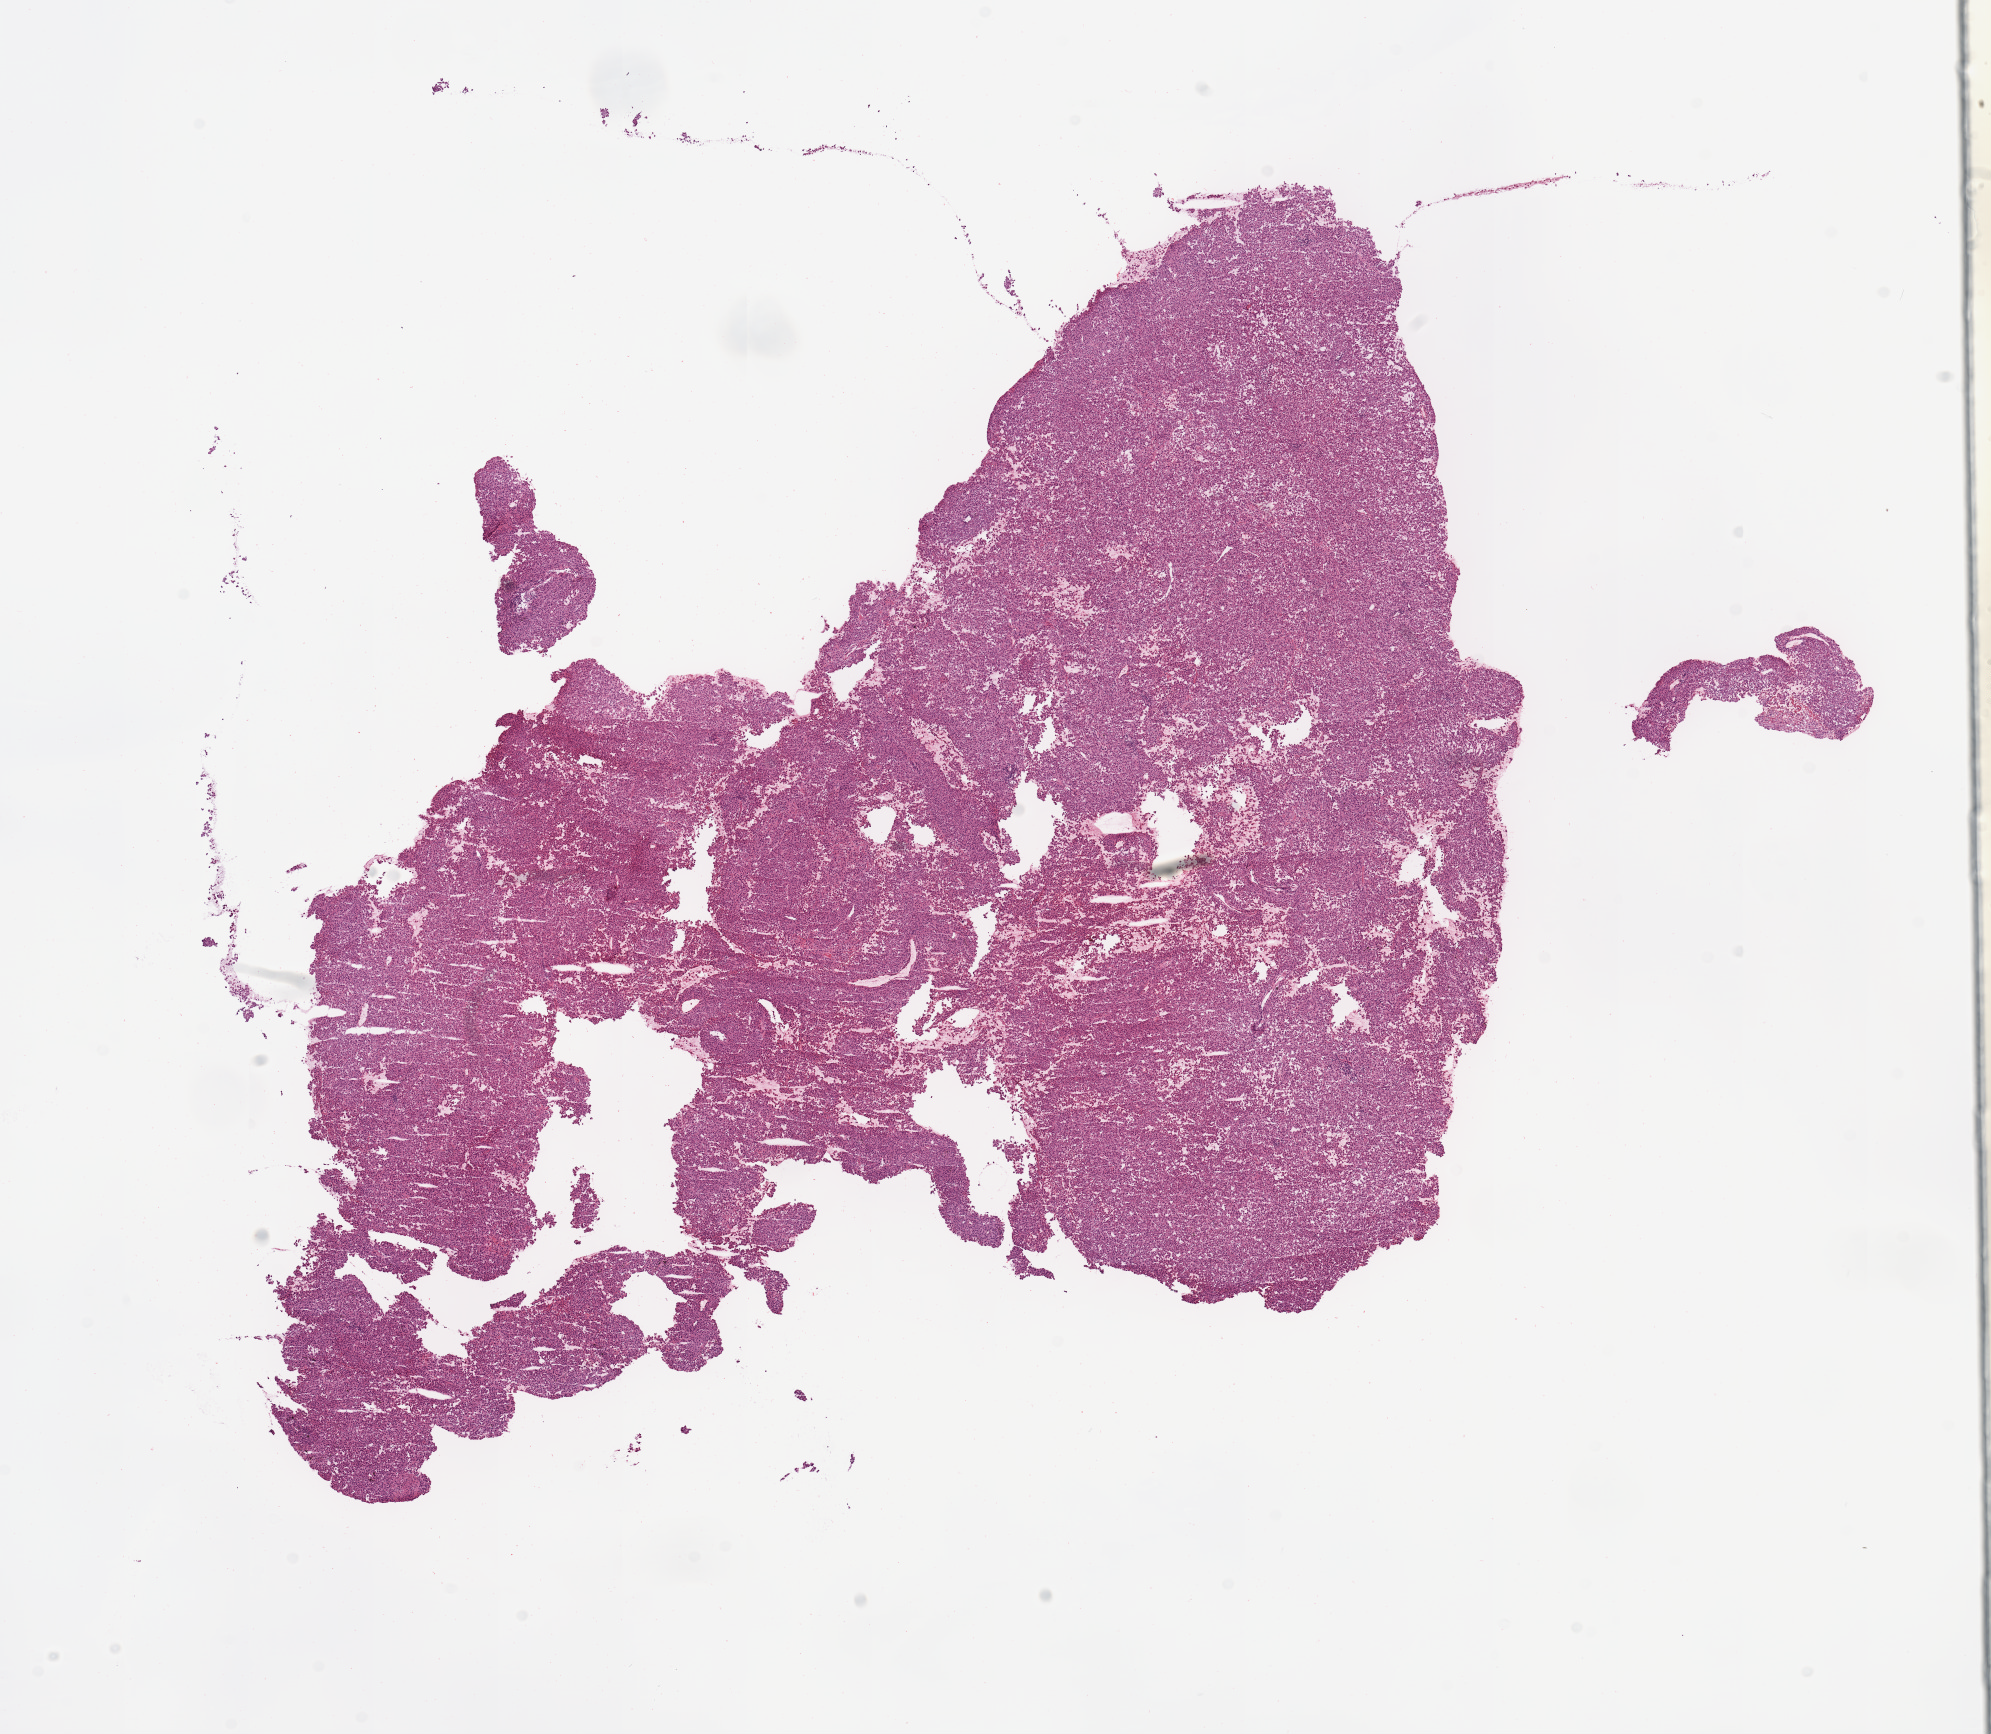
Digitized Hematoxylin and eosin (H&E) stained tissue section (whole slide), whole scanned area (about 15.8 x 13.7 mm, from a 20x scan) shown as a low-resolution overview. Melanoma tumour tissue; sampled site not recorded. Male, 51 y/o.
Patient diagnosis (cohort enrolment): cutaneous melanoma (skin).